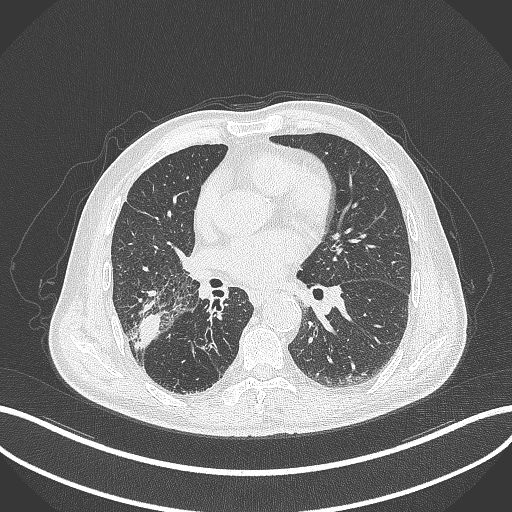
Chest CT, one axial slice. 120 kVp. Lung window (W 1500 / L -600 HU). 1 mm slice thickness. 512 × 512 image matrix, field of view 400 × 400 mm. Male patient, age 72 years. Case-level facts recorded for this patient, not image findings: clinical TNM (as recorded): T3 N2 M0.
Annotated regions visible in this slice (bounding box drawn by a radiologist):
- lung tumour (recorded histology: adenocarcinoma): bounding box (x1, y1, x2, y2) in pixels: (127, 310, 166, 355)